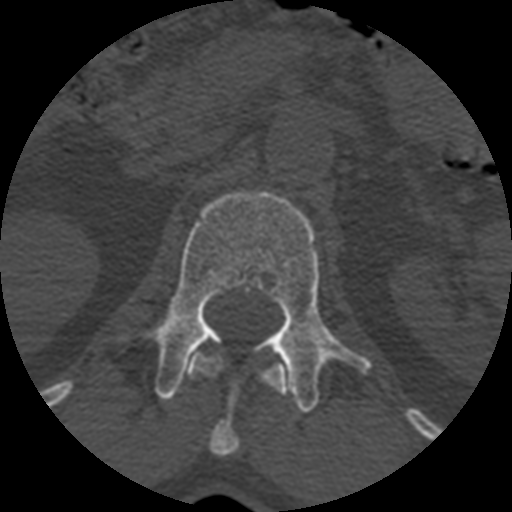
CT including the spine, one axial slice. Slice 366 of 399 in the series (ordered by position). Reconstruction kernel STANDARD. Bone window (W 1800 / L 400 HU). 1.25 mm slice thickness. 512 × 512 image matrix, field of view 160 × 160 mm. Patient age 71 years. From the clinical record (not read from this slice): primary cancer: prostate.
Outlined on this slice (semi-automatic segmentation, software-assisted and operator-edited):
- L1 vertebra: box from (x=119, y=190) to (x=372, y=411) px
- T12 vertebra: (x=186, y=349)–(x=286, y=457)